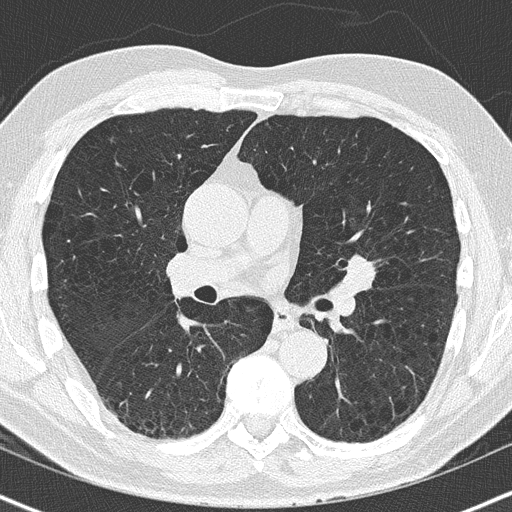
Low-dose screening chest CT, one axial slice. Slice 86 of 163 in the series (ordered by position). 120 kVp. Lung window (W 1500 / L -600 HU). 2 mm slice thickness. 512 × 512 image matrix.
Annotated regions visible in this slice (expert manual segmentation):
- lesion 1 (tumor, upper lobe of left lung): bounding box <343,254,376,296> (left, top, right, bottom; pixels)